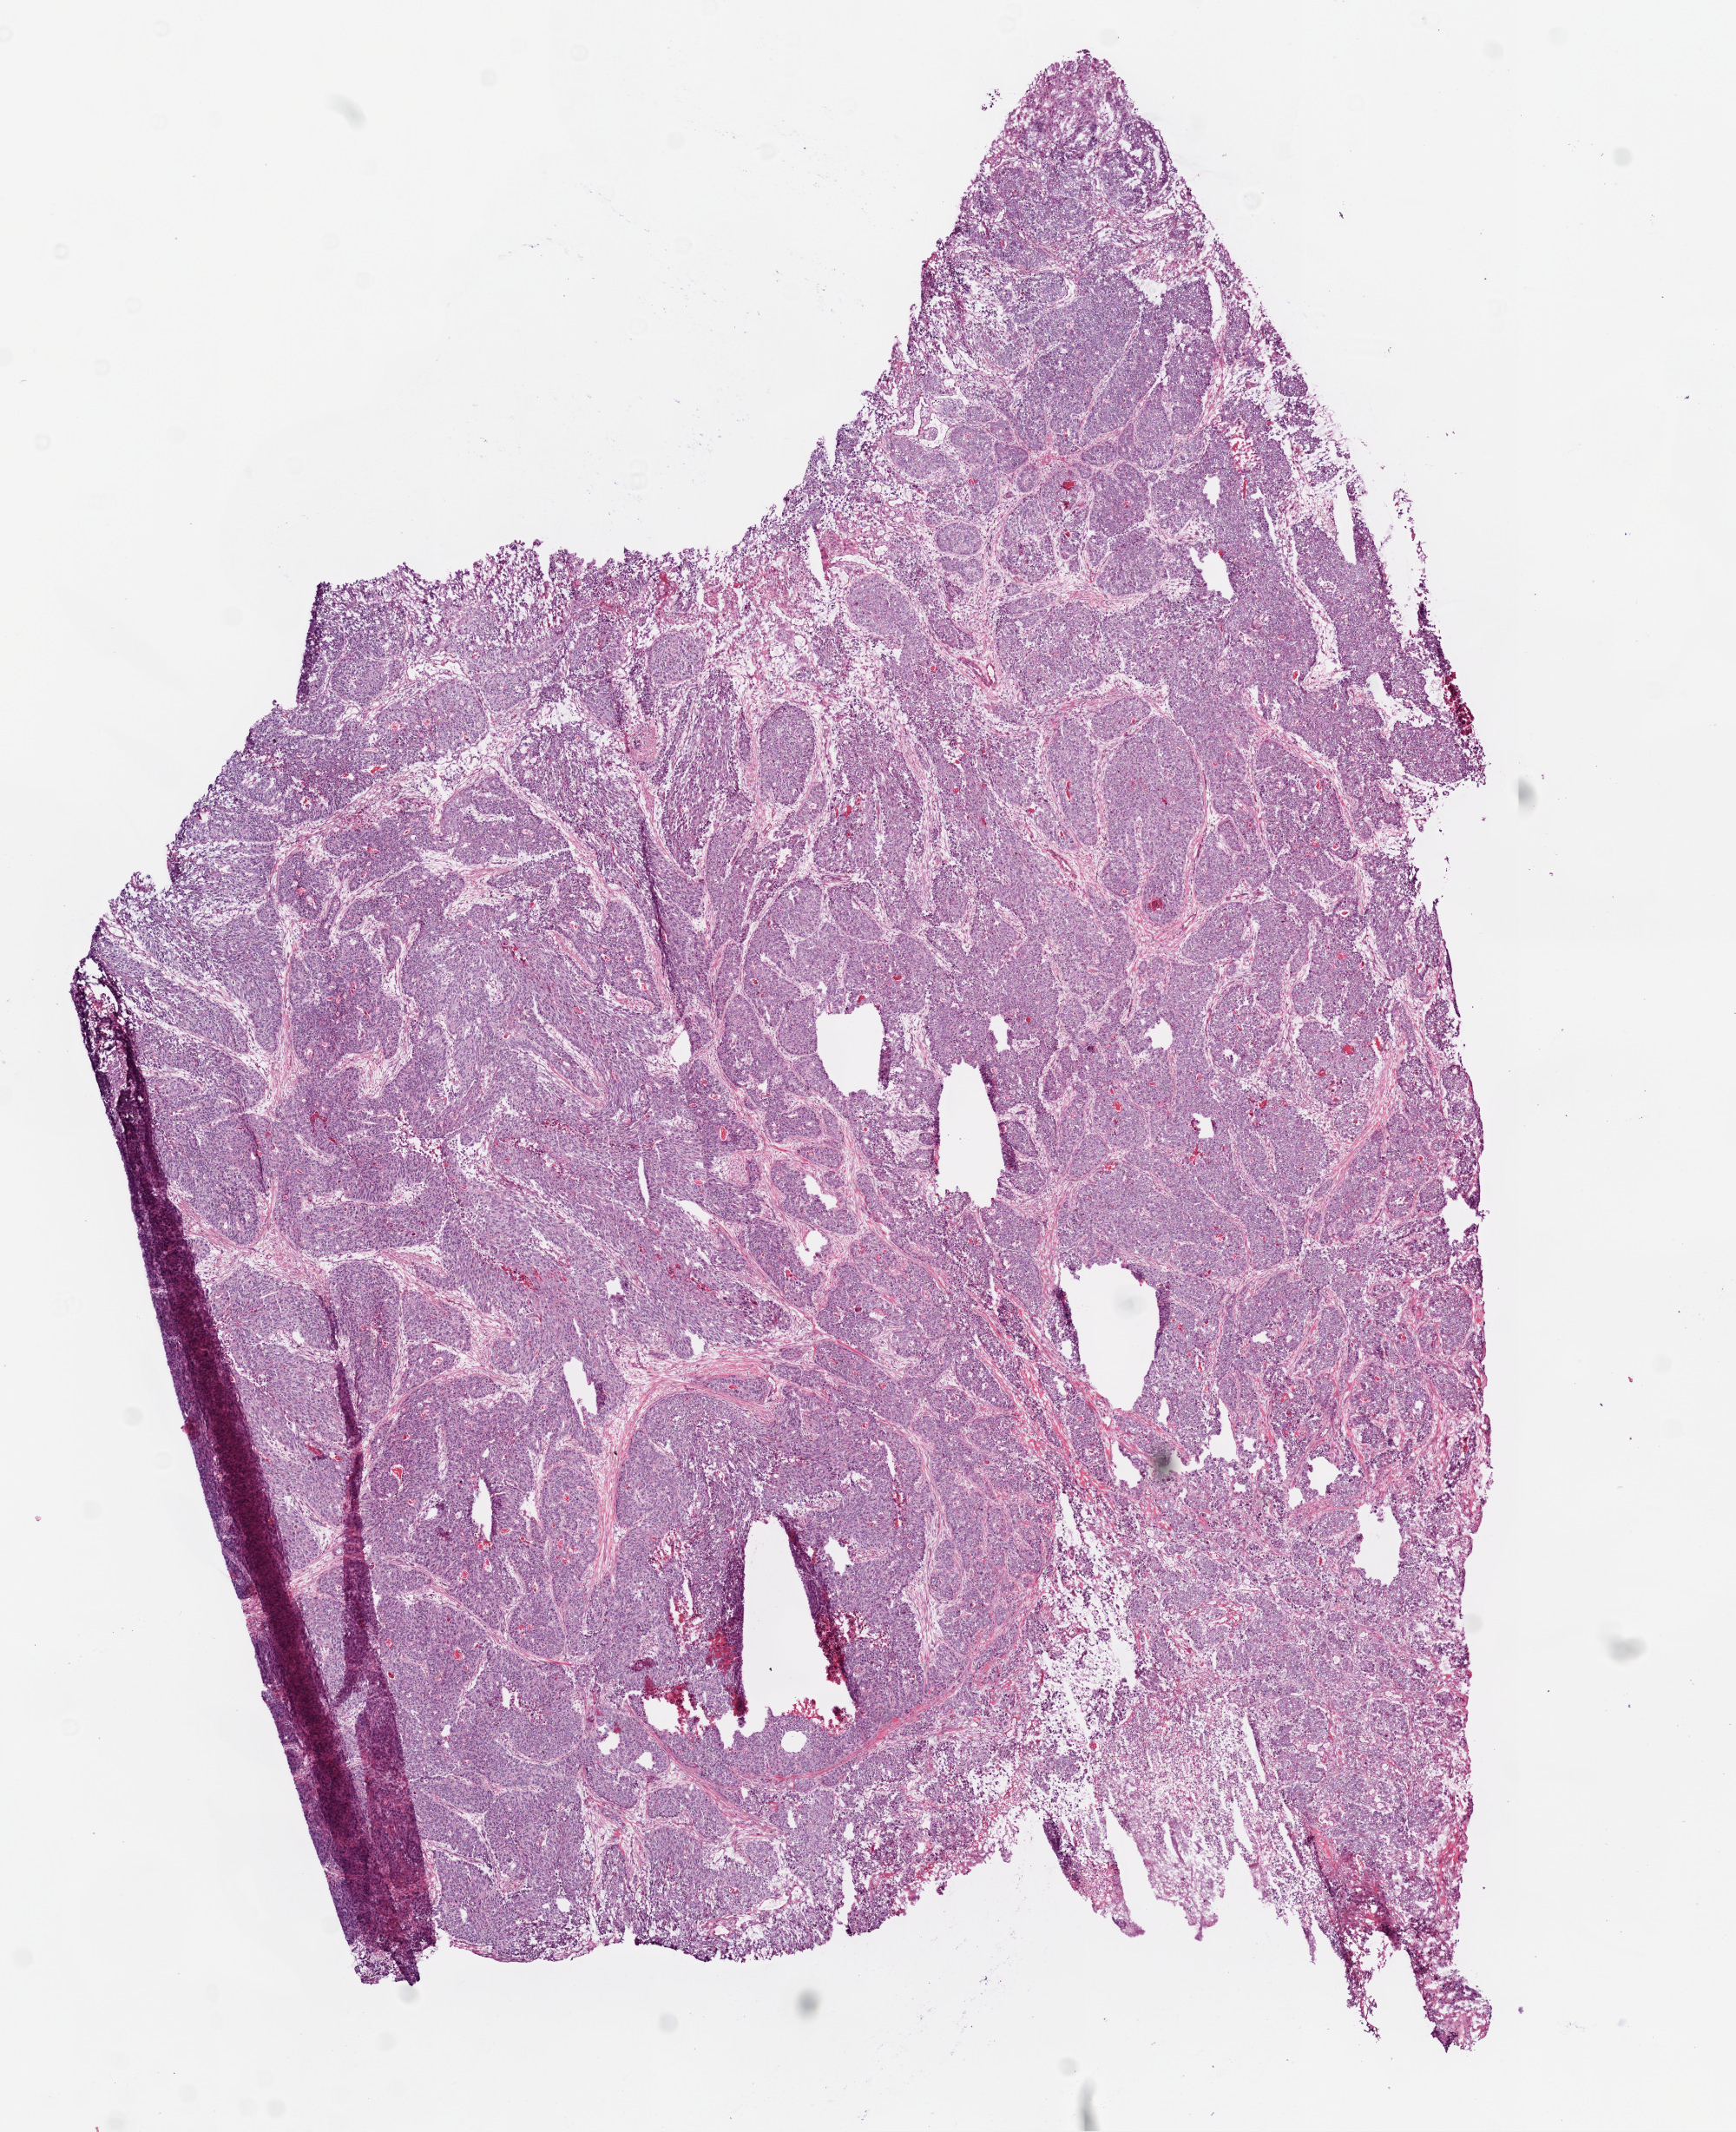
Whole-slide histology image, H&E, low-resolution overview of the scanned area, about 8.0 x 9.9 mm (from a 20x scan), frozen section, colon, primary tumour sample. Male, age 69 years at initial diagnosis. Composition of this section per pathologist review: tumour cells 80%, tumour nuclei 90%, normal cells 0%, stromal cells 13%, necrosis 7%.
Histologic diagnosis: Adenocarcinoma, NOS (sigmoid colon). AJCC pathologic stage: IIIC (6th edition).